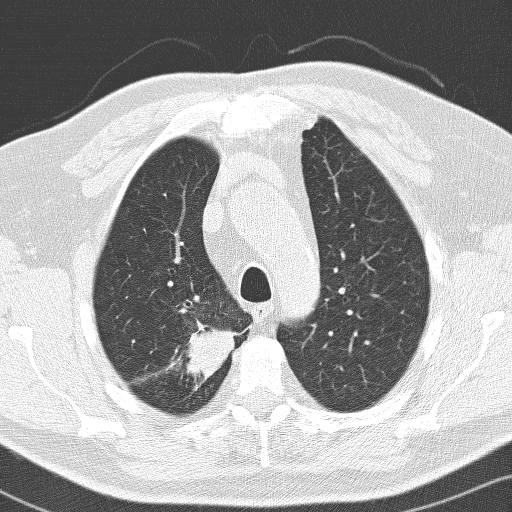
Low-dose screening chest CT, one axial slice; slice 112 of 141 in the series (ordered by position); lung window (W 1500 / L -600 HU); 512 × 512 image matrix, field of view 326 × 326 mm.
Outlined on this slice (manually delineated by an expert):
- lesion 1 (tumor, upper lobe of right lung): bounding box [x1, y1, x2, y2] px = [187, 321, 238, 383]